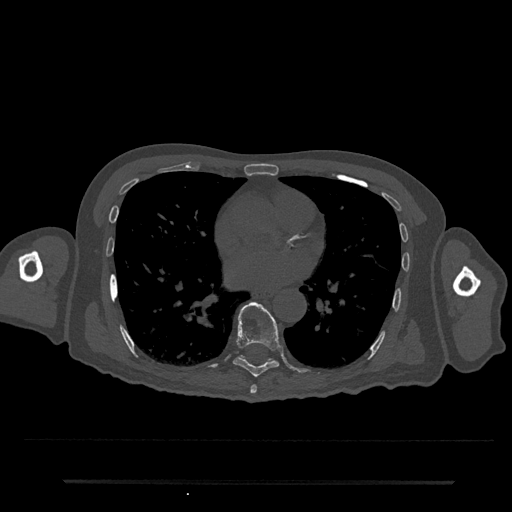
CT including the spine, one axial slice. Slice 415 of 797 in the series (ordered by position). Reconstruction kernel Br40s/3. 120 kVp. Bone window (W 1800 / L 400 HU). 0.5 mm slice thickness. 512 × 512 image matrix. Patient: male, 74 years. Case-level facts recorded for this patient, not image findings: primary cancer: prostate.
Structures marked on this image (semi-automatic segmentation, software-assisted and operator-edited):
- T7 vertebra: bounding box (x1, y1, x2, y2) in pixels: (250, 385, 257, 394)
- T8 vertebra: (233, 302, 281, 377)
- T9 vertebra: (240, 356, 273, 361)